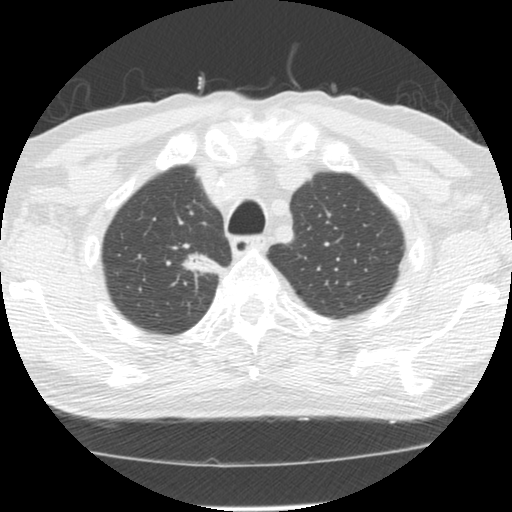
Axial slice from a low-dose chest CT screening exam, baseline screening round, lung window (W 1500 / L -600 HU), 2.5 mm slice thickness, 120 kVp. Male participant, aged 64 years at enrolment.
Expert reader's lesion annotation, bounding box [x1, y1, x2, y2] px = [176, 237, 224, 279]. The exam's reader record, not a measurement of the box and not confirmed to be the same lesion: non-calcified nodule or mass ≥4 mm, right upper lobe, 20 × 13 mm, spiculated (stellate) margins, soft tissue attenuation. Official screen result: positive, change unspecified: nodule(s) >= 4 mm or enlarging nodule(s), mass(es), or other non-specific abnormalities suspicious for lung cancer. Lung cancer was diagnosed 73 days after this screen: adenocarcinoma, NOS, right upper lobe, moderately differentiated (G2), stage IA (AJCC 6th edition), 17 mm at pathology.